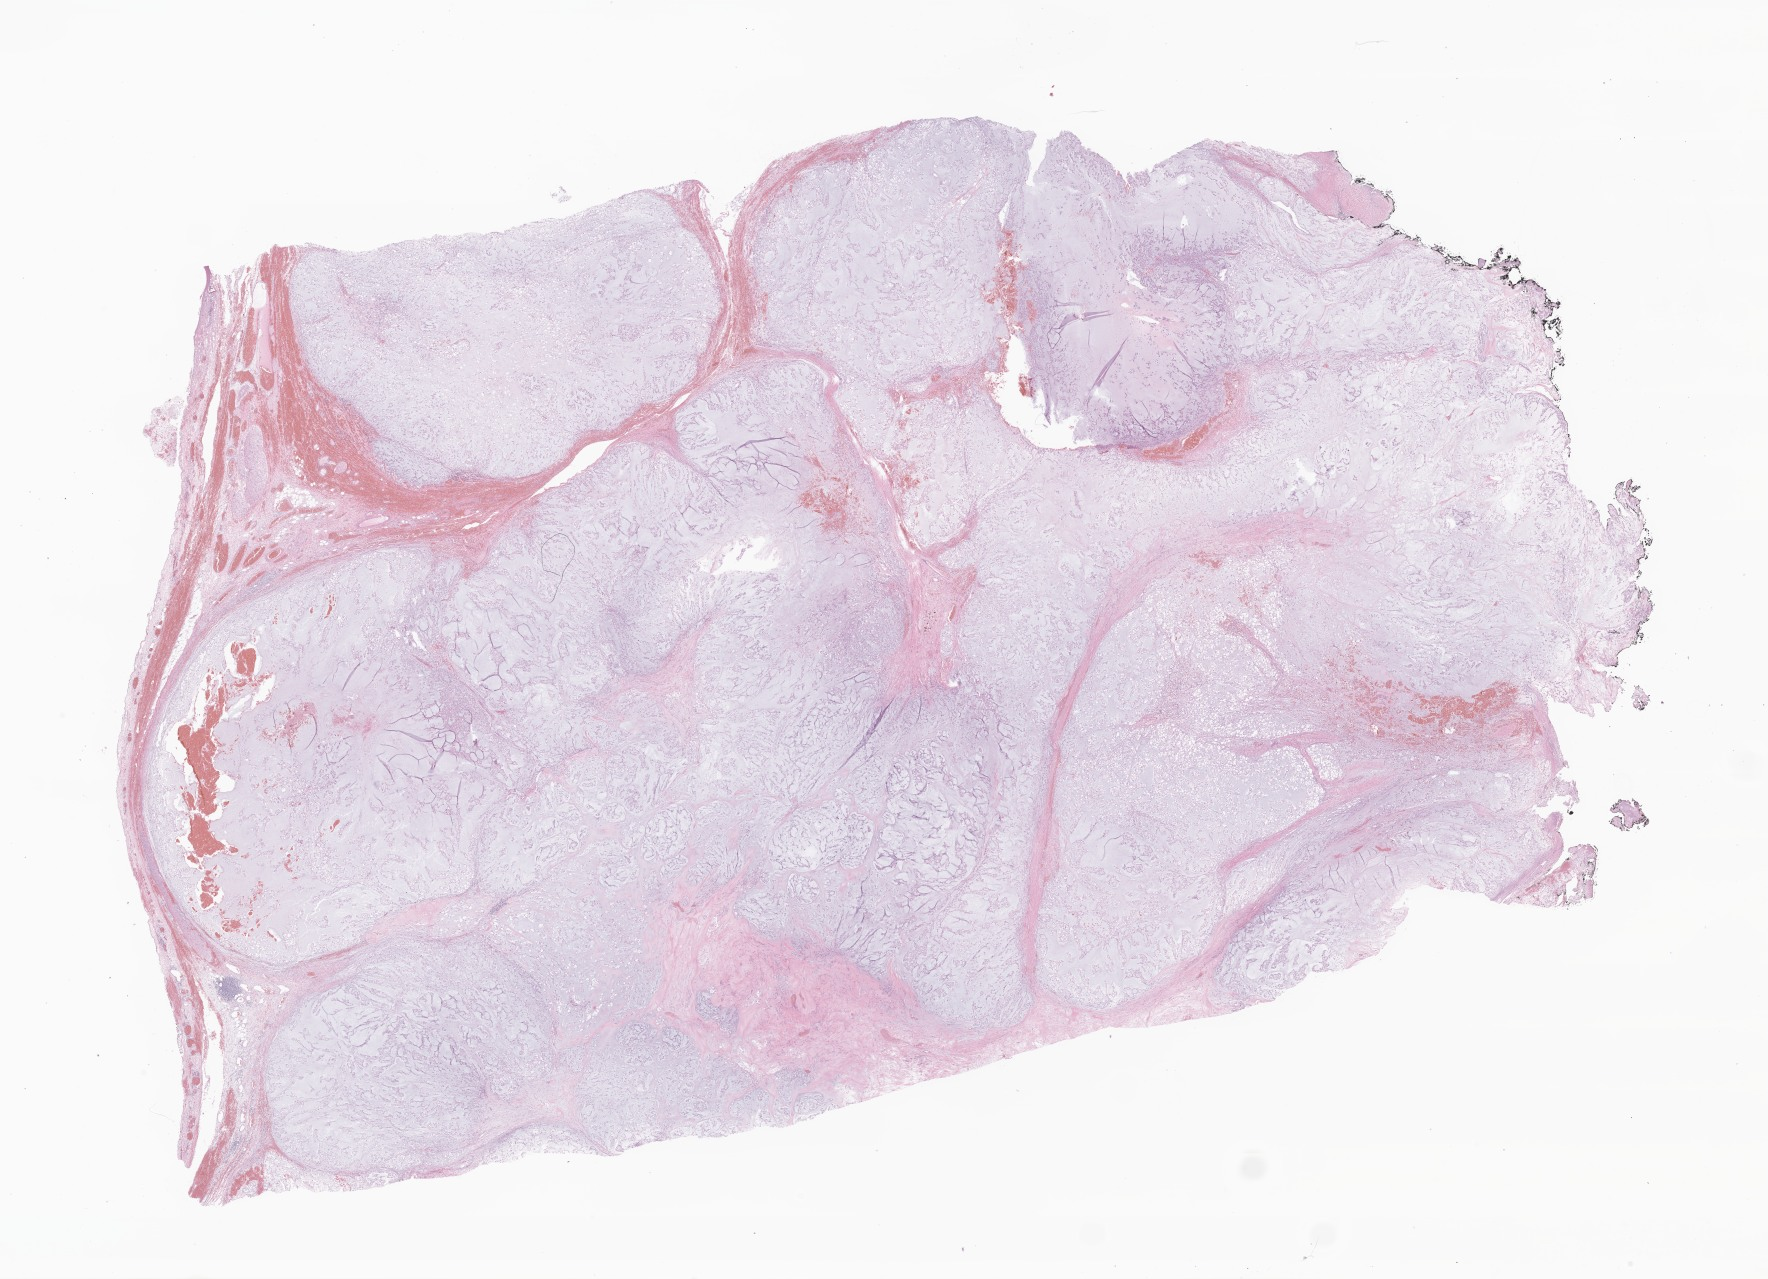
Whole-slide image, haematoxylin and eosin stain of tumor tissue from the mediastinum — shown as a low-resolution overview of the whole scanned area (about 29.8 x 21.6 mm), formalin-fixed paraffin-embedded section. Patient female; age 136 months (11 years 4 months).
Recorded diagnosis: Chordoma, NOS.